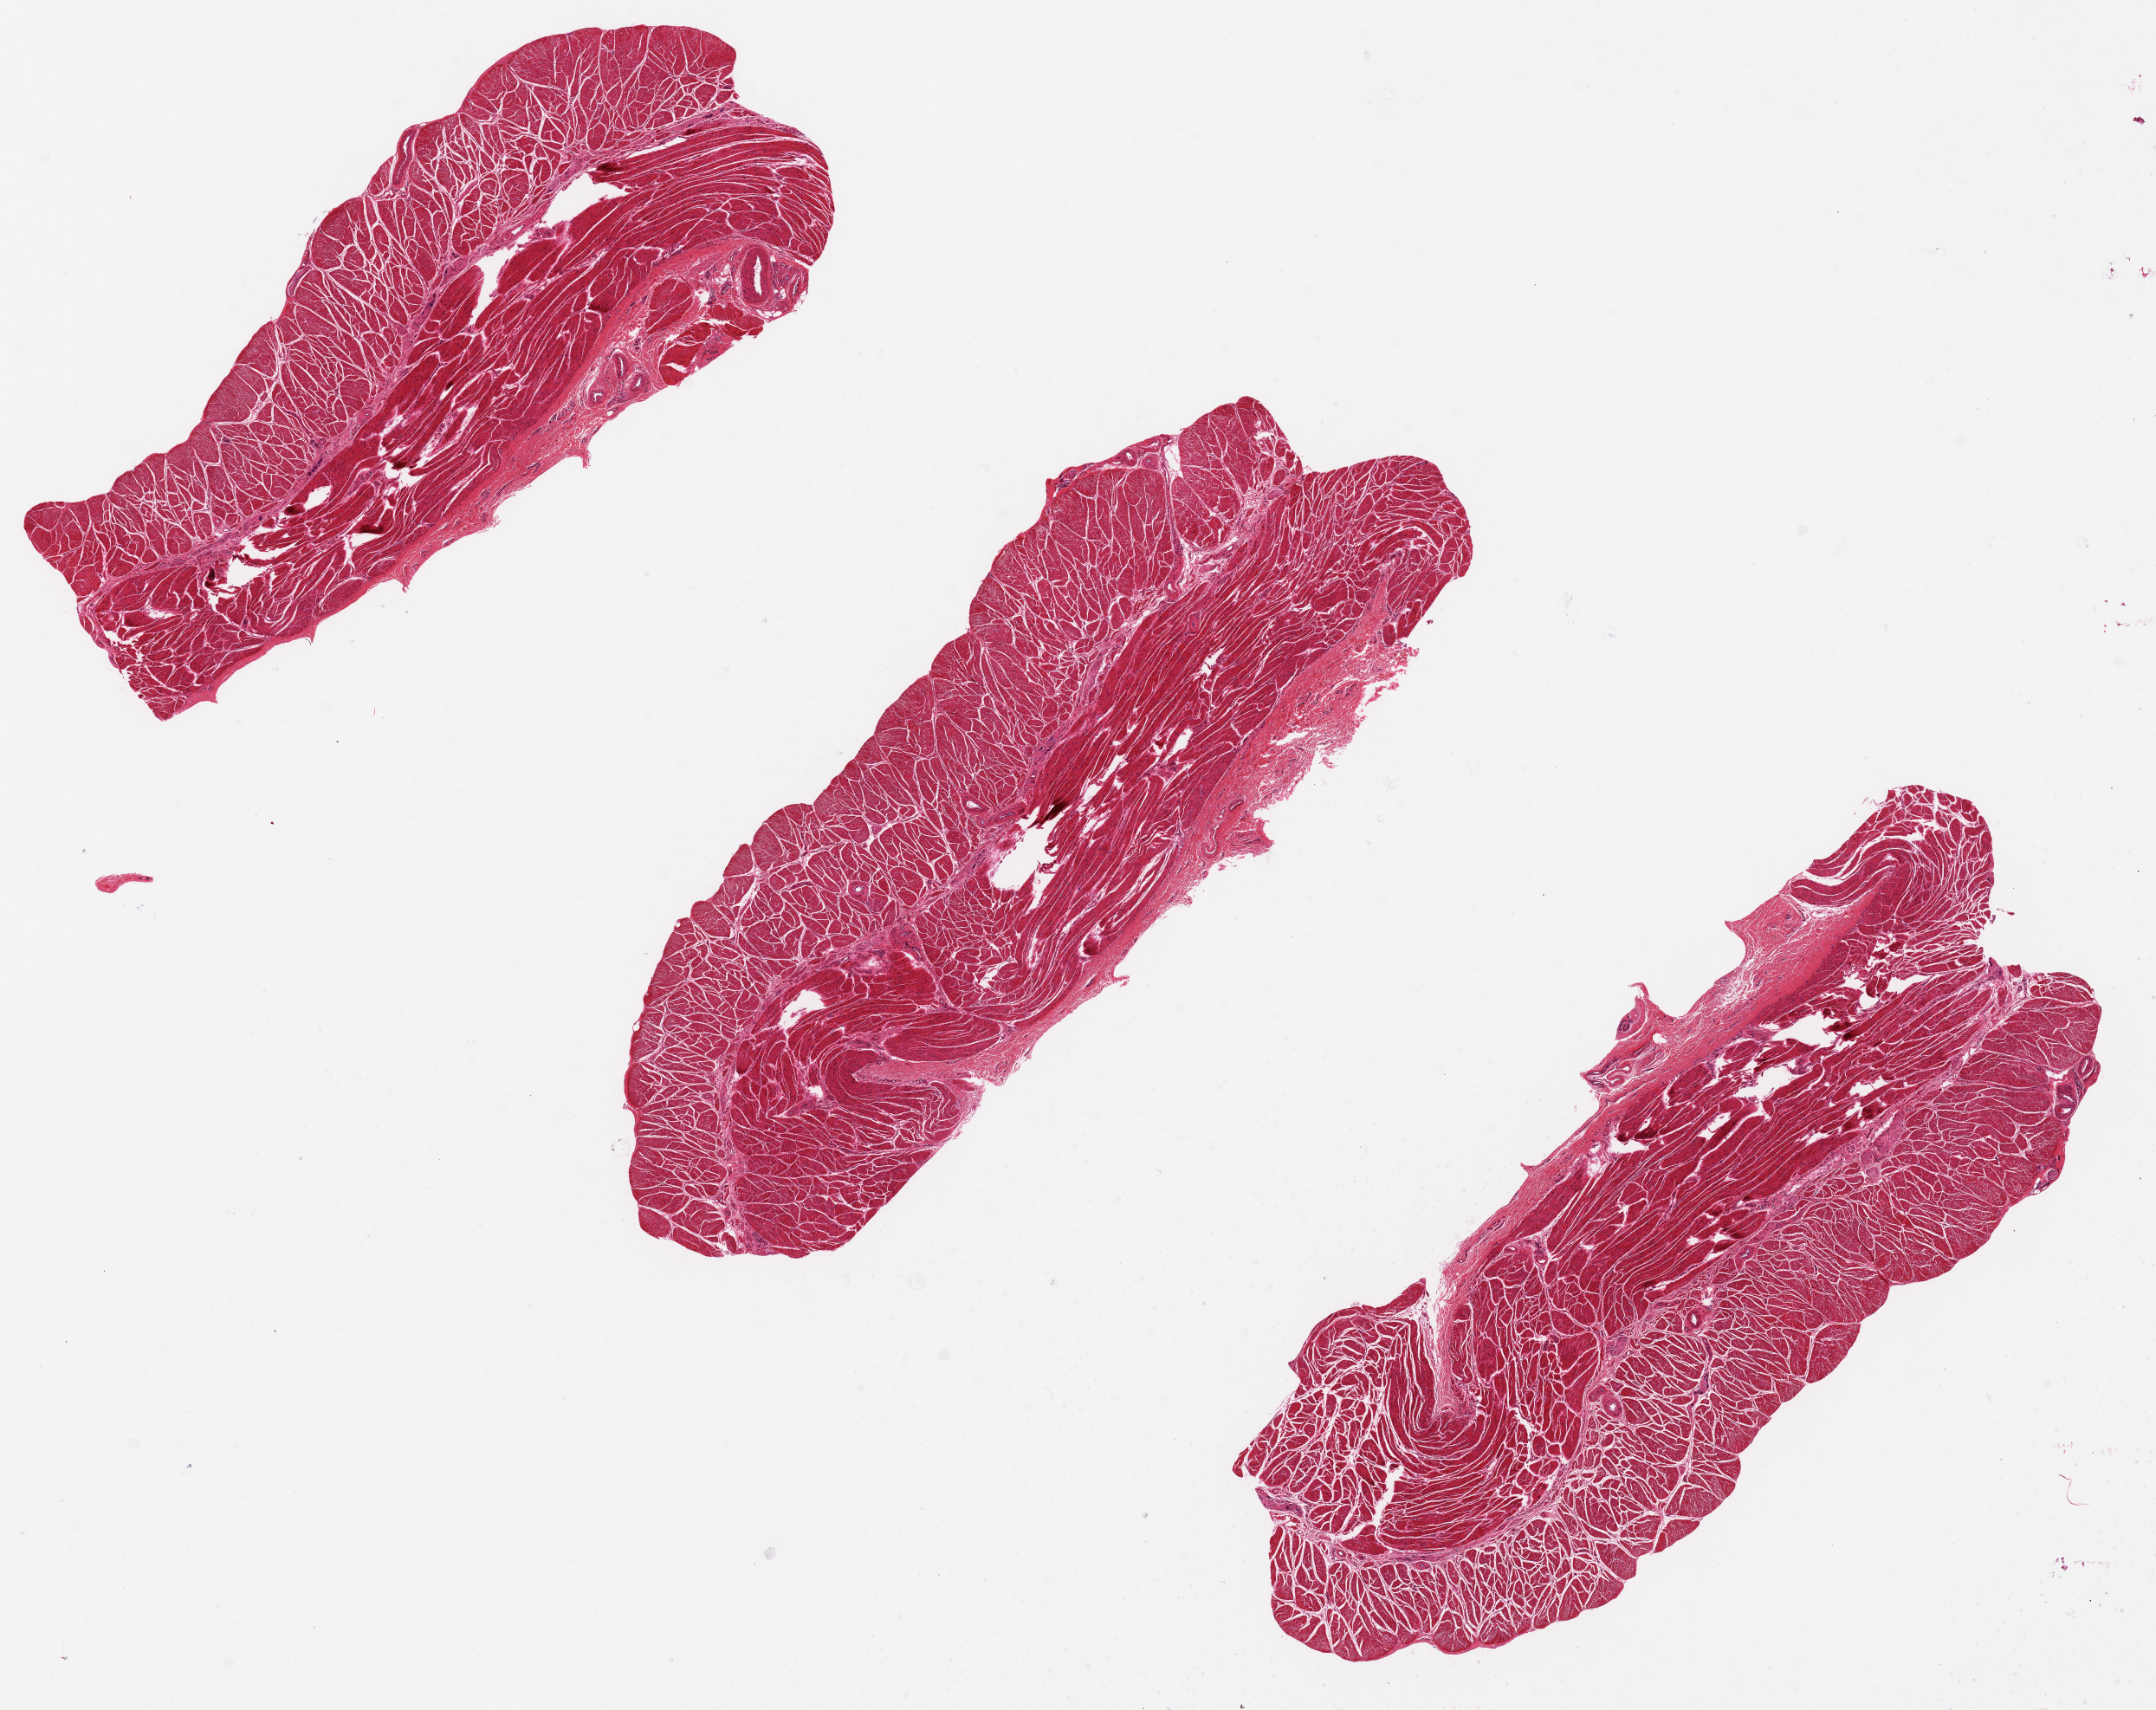
Digitized haematoxylin and eosin-stained section, whole scanned area (about 19.7 x 15.6 mm) shown as a low-resolution overview. PAXgene-fixed paraffin-embedded (PFPE) section. Target tissue: esophageal muscle. Donor tissue sample. Male donor.
Review note (as recorded): OK for analysis.